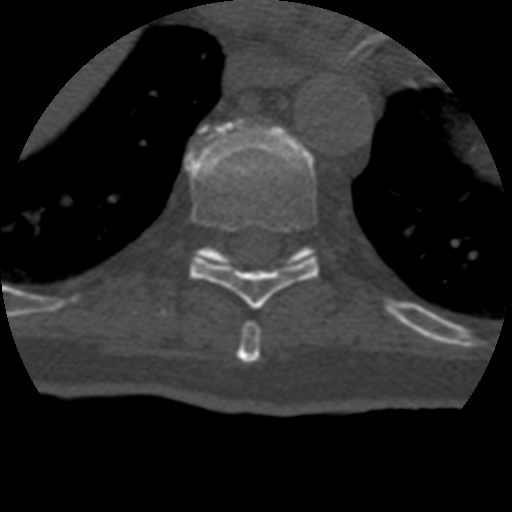
CT including the spine, one axial slice; position 235 of 399 along the scan axis; bone window (W 1800 / L 400 HU); 512 × 512 image matrix. Patient age 69 years. Case-level facts recorded for this patient, not image findings: primary cancer: prostate.
Outlined on this slice (semi-automatically segmented with operator editing):
- T10 vertebra: box from (x=197, y=131) to (x=315, y=266) px
- T8 vertebra: (x=237, y=322)–(x=262, y=363)
- T9 vertebra: (x=188, y=125)–(x=320, y=310)